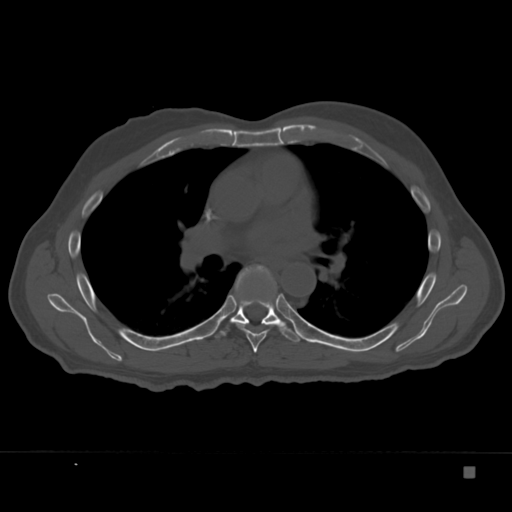
CT including the spine, one axial slice; slice 232 of 332 in the series (ordered by position); reconstruction kernel Br40s; 120 kVp; bone window (W 1800 / L 400 HU); 512 × 512 image matrix, field of view 389 × 389 mm. Male patient, age 72 years. Case-level facts recorded for this patient, not image findings: primary cancer: skeletal.
Annotated regions visible in this slice (semi-automatic segmentation, software-assisted and operator-edited):
- T6 vertebra: box from (x=235, y=265) to (x=279, y=353) px
- T7 vertebra: (x=212, y=267)–(x=302, y=343)